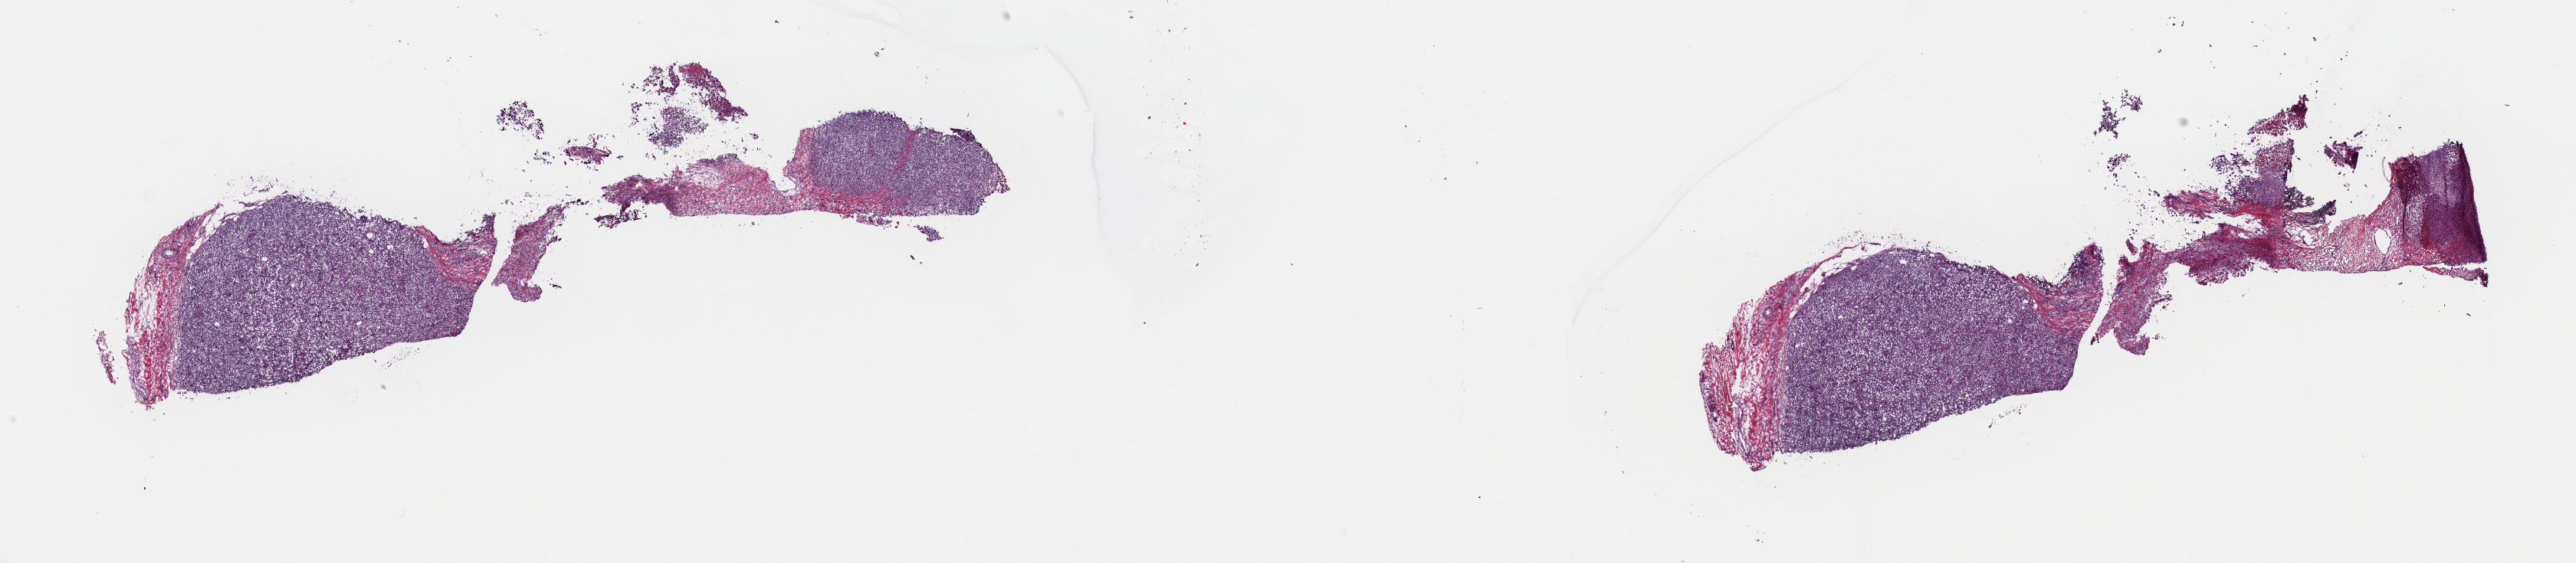
Digitized H&E-stained tissue section (whole slide), a low-resolution overview of the entire scanned area, about 26.5 x 5.8 mm. Frozen section. Metastatic tumour sample, sampled site not recorded. Patient: female, age at initial diagnosis 48 years. Composition of this section per pathologist review: tumour cells 60%, tumour nuclei 70%, normal cells 10%, stromal cells 30%, necrosis 0%. Infiltration values recorded for this section: lymphocyte infiltration 0%, monocyte infiltration 0%, neutrophil infiltration 0%.
• this section: metastatic tumour tissue
• patient diagnosis: Malignant melanoma, NOS